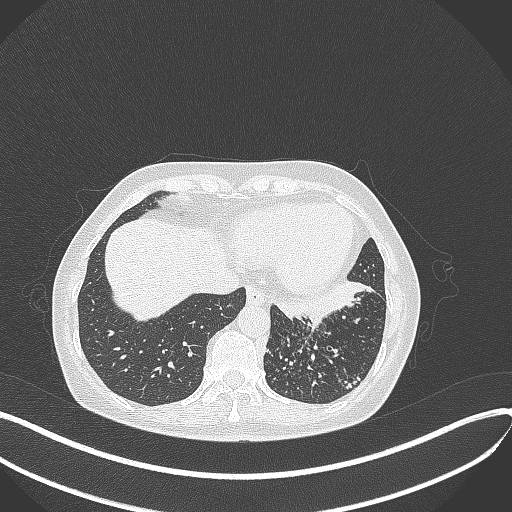
Chest CT, one axial slice. Position 104 of 429 along the scan axis. Reconstruction kernel B70f. 100 kVp. Lung window (W 1500 / L -600 HU). 1 mm slice thickness. 512 × 512 image matrix, field of view 400 × 400 mm. Female patient, age 63 years. Case-level facts recorded for this patient, not image findings: clinical TNM (as recorded): T1b N0 M0; histopathological grade: G2-3.
Annotated regions visible in this slice (rectangle marked by the reading radiologist):
- lung tumour (recorded histology: adenocarcinoma): bounding box (x1, y1, x2, y2) in pixels: (274, 273, 375, 327)